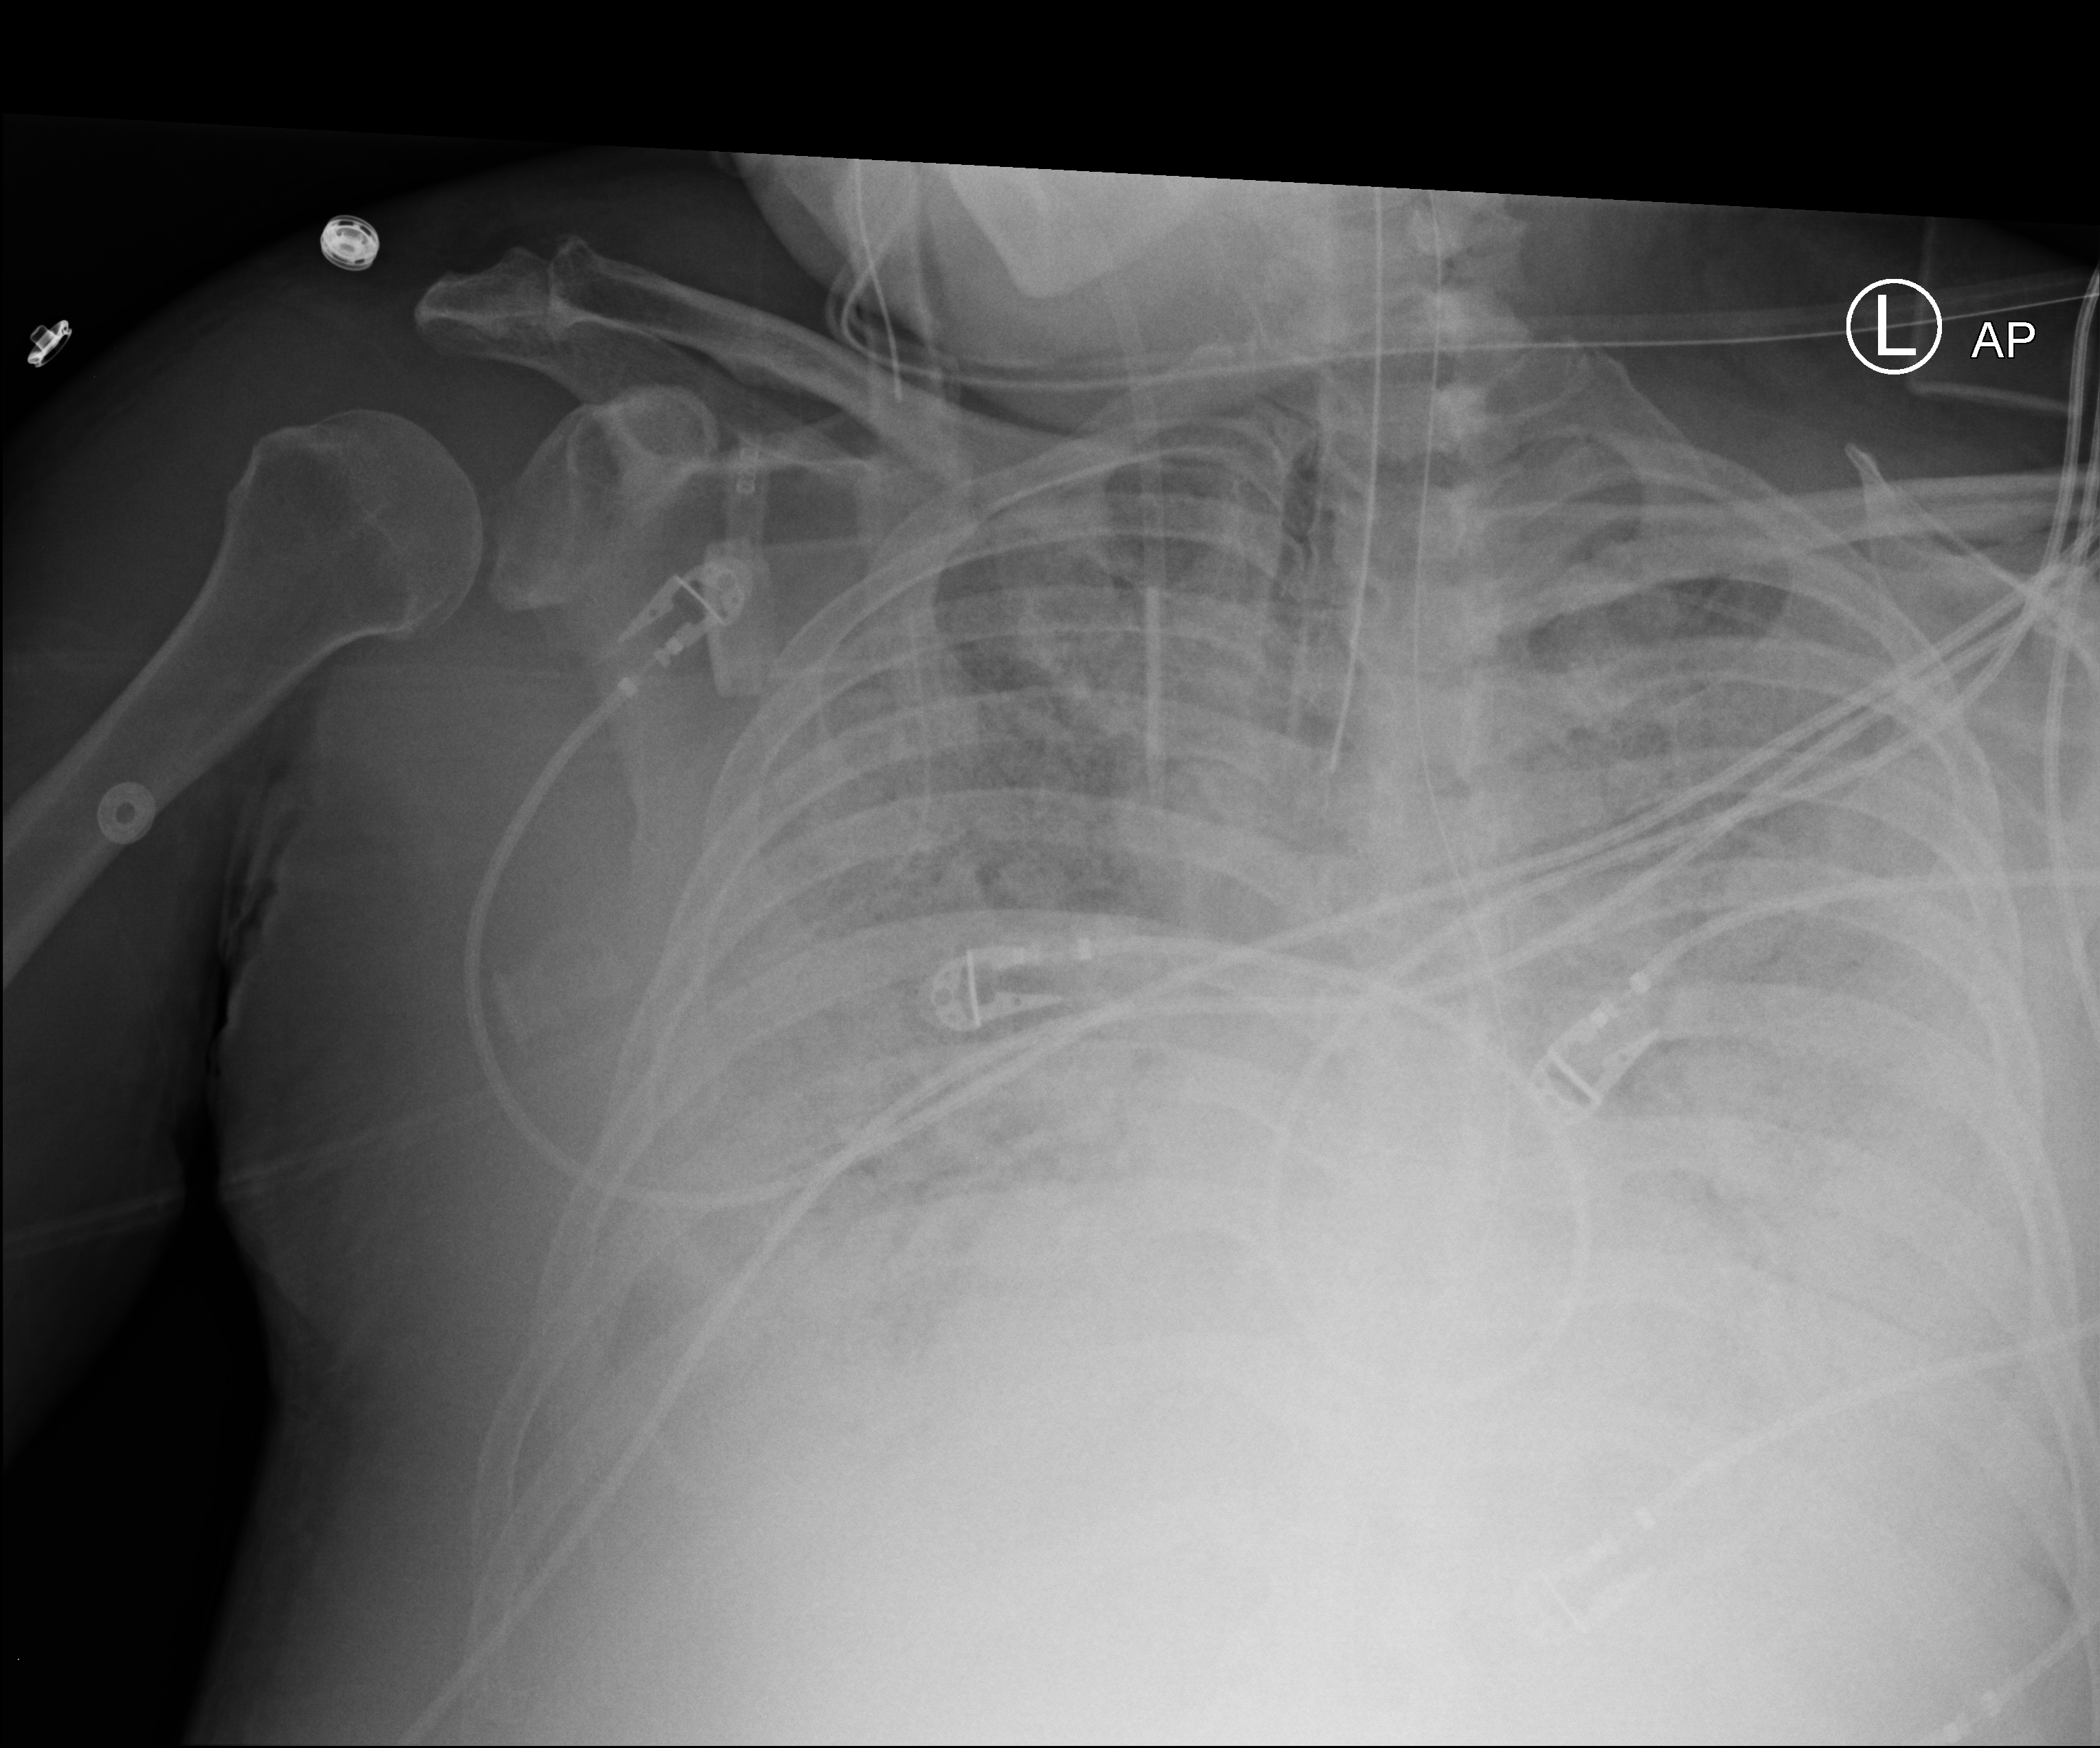
Bedside chest radiograph (computed radiography). Patient hospitalised with COVID-19; male, aged 60–74 years.
From the hospital-stay record, not from the radiograph (when in the stay this image was taken is not recorded): length of hospital stay: 28 days; admitted to intensive care during this hospital stay: yes.